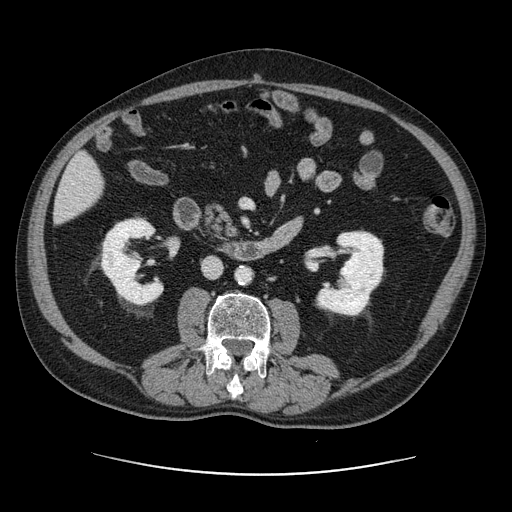
Contrast-enhanced abdominal CT, one axial slice; slice 35 of 141 in the series (ordered by position); 120 kVp; intravenous contrast given; soft-tissue window (W 400 / L 40 HU); 2.5 mm slice thickness; 512 × 512 image matrix, field of view 395 × 395 mm. Male patient, age 72 years. From the clinical record (not read from this slice): diagnosis: colorectal cancer liver metastases, imaged before liver resection; multiple liver metastases: yes; largest metastasis: 5.4 cm; chemotherapy before resection: yes.
Annotated regions visible in this slice (expert manual segmentation):
- liver: bounding box <55,154,104,223> (left, top, right, bottom; pixels)
- planned liver remnant (the part of the liver to remain after resection): <55,154,104,223>